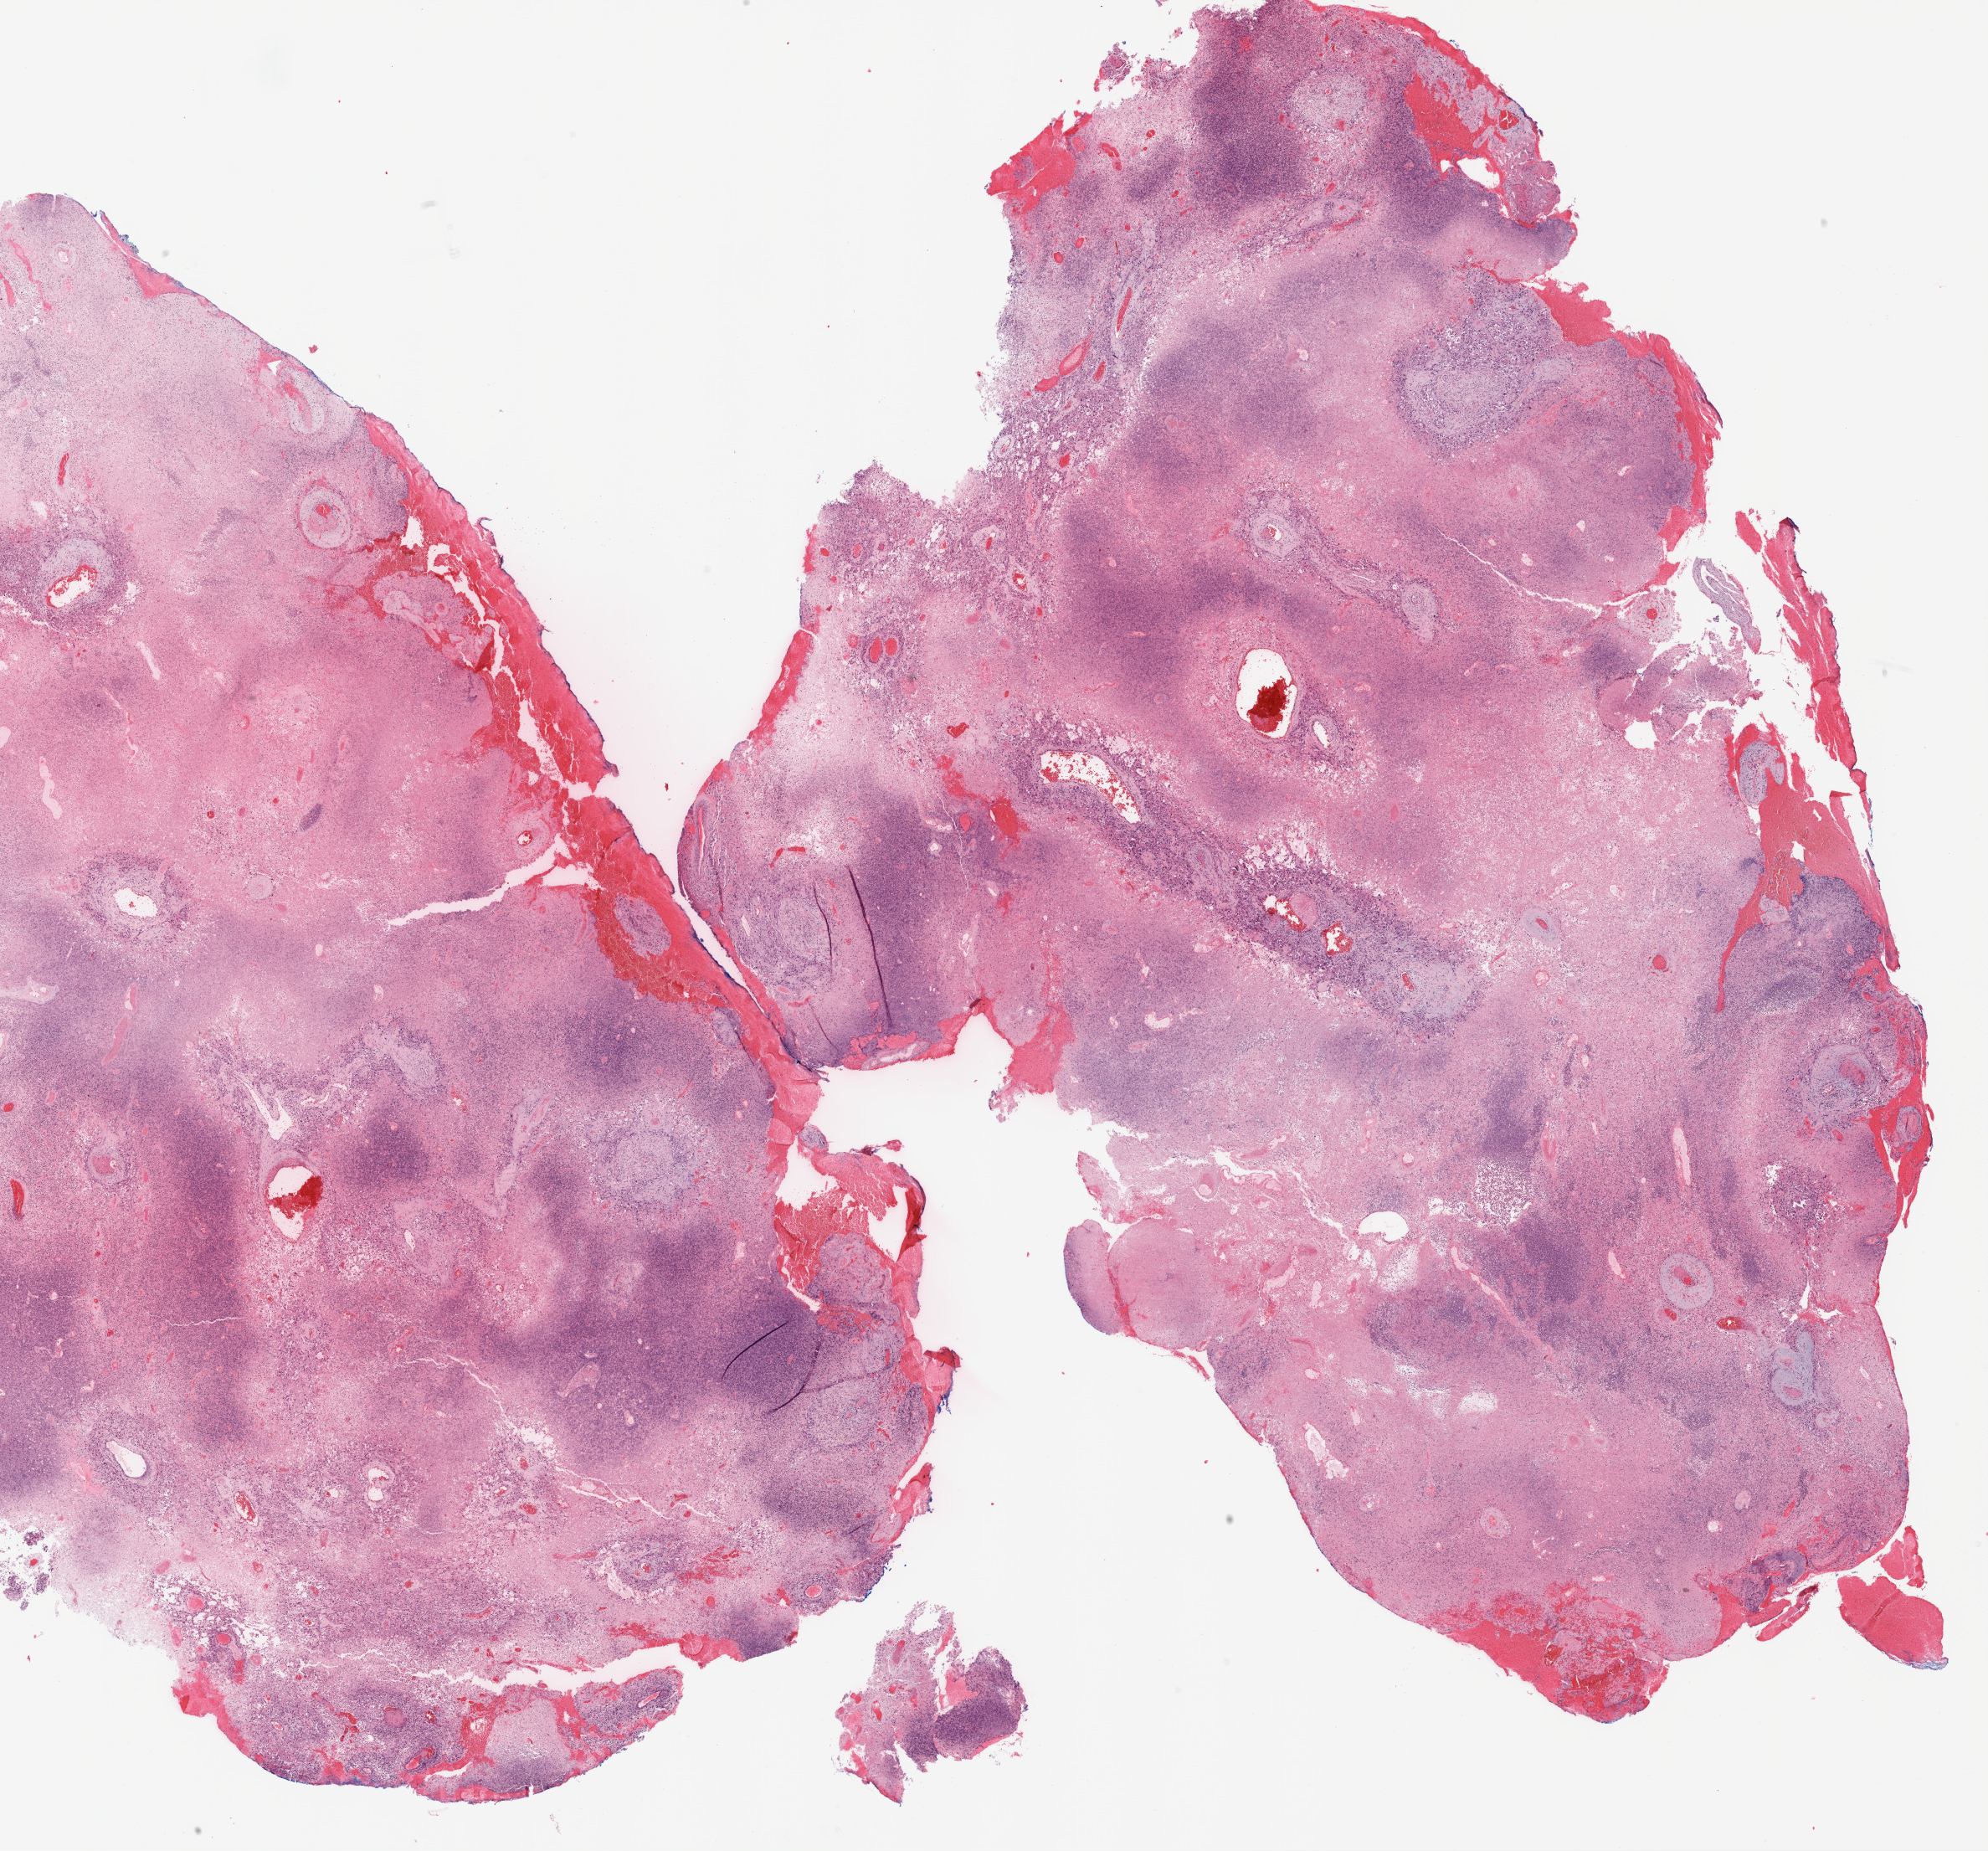
Digitized Hematoxylin and eosin (H&E) stained tissue section (whole slide), a low-resolution overview of the entire scanned area, about 19.1 x 17.7 mm, formalin-fixed paraffin-embedded (FFPE) diagnostic section, brain, primary tumour sample. Male, age 66 years at initial diagnosis.
- pathologic diagnosis: Glioblastoma